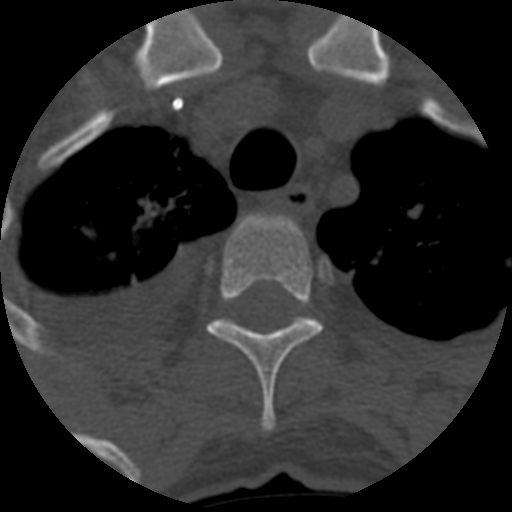
CT including the spine, one axial slice. Position 487 of 708 along the scan axis. Reconstruction kernel STANDARD. 120 kVp. One of 3 acquisitions stored at this slice position. Bone window (W 1800 / L 400 HU). 1.25 mm slice thickness. 512 × 512 image matrix, field of view 160 × 160 mm. Patient age 55 years. Case-level facts recorded for this patient, not image findings: primary cancer: colon.
Annotated regions visible in this slice (semi-automatic segmentation, software-assisted and operator-edited):
- T3 vertebra: bounding box [x1, y1, x2, y2] px = [207, 213, 323, 432]
- T4 vertebra: [217, 316, 316, 329]